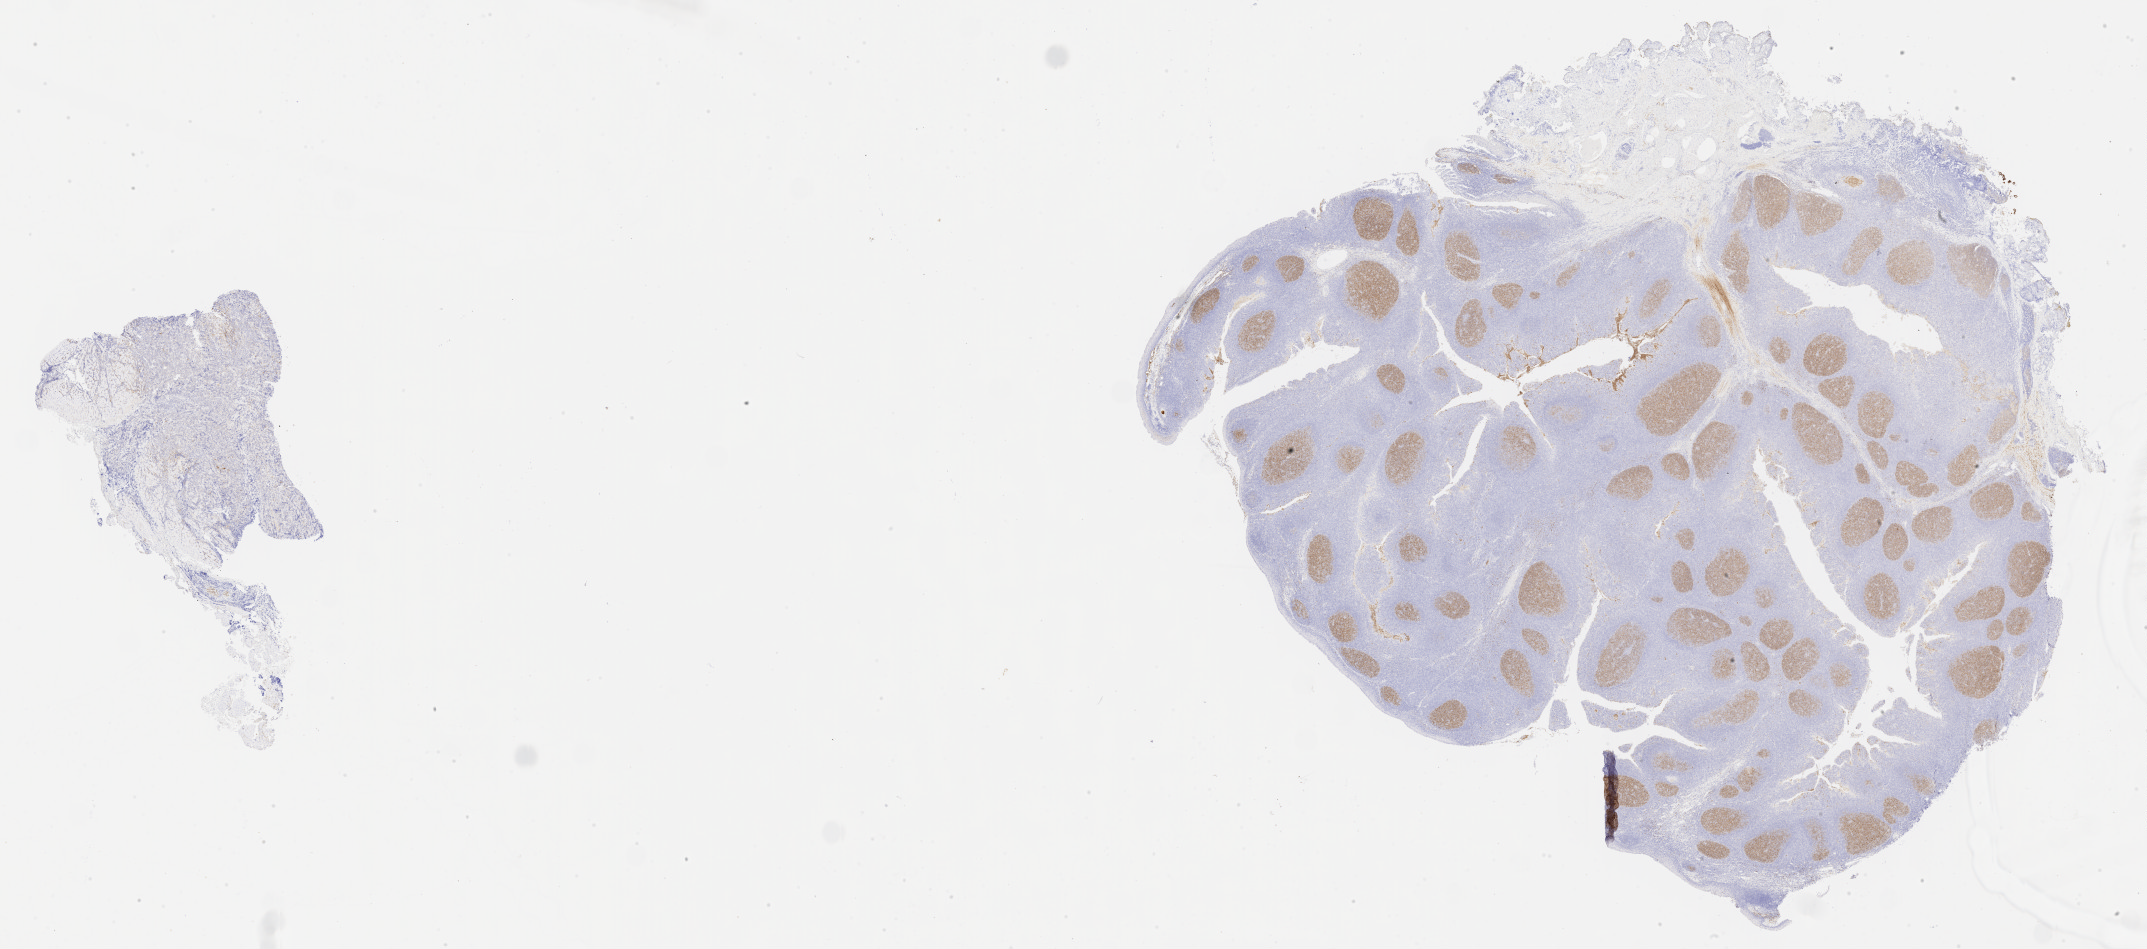
IHC for CD10, whole-slide image — shown as a low-resolution overview of the whole scanned area (about 34.7 x 15.3 mm); tumor tissue; anatomic site: kidney. Patient: male, 12 years old.
Diagnosis: Diffuse large B-cell lymphoma, NOS.